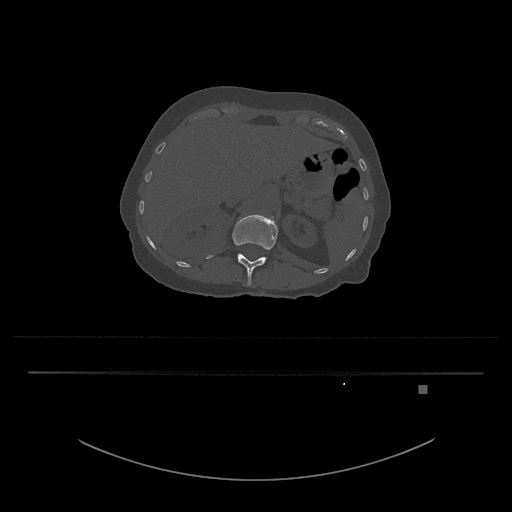
CT including the spine, one axial slice; position 546 of 797 along the scan axis; reconstruction kernel Br40s/3; bone window (W 1800 / L 400 HU); 0.5 mm slice thickness; 512 × 512 image matrix, field of view 500 × 500 mm. Patient: female, 57 years. From the clinical record (not read from this slice): primary cancer: cervical.
Outlined on this slice (semi-automatic segmentation, software-assisted and operator-edited):
- L1 vertebra: box from (x=207, y=215) to (x=278, y=286) px